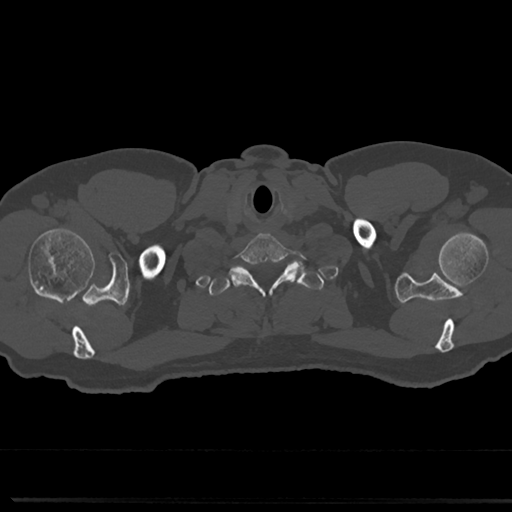
CT including the spine, one axial slice. Slice 692 of 817 in the series (ordered by position). Reconstruction kernel Br40s/3. 120 kVp. Bone window (W 1800 / L 400 HU). 0.5 mm slice thickness. 512 × 512 image matrix. Male patient, age 61 years. From the clinical record (not read from this slice): primary cancer: prostate.
Structures marked on this image (semi-automatic segmentation, software-assisted and operator-edited):
- T1 vertebra: bounding box (x1, y1, x2, y2) in pixels: (210, 262, 318, 342)